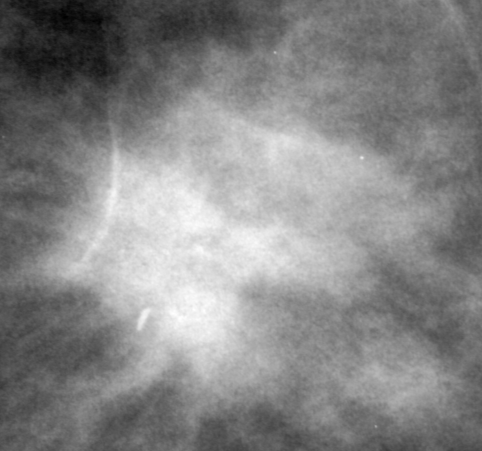
Cropped region of a digitized screen-film mammogram centred on a radiologist-marked abnormality, right breast, CC view.
Mass, shape irregular, margins obscured; BI-RADS assessment category 3; subtlety rating 3 on a 1 (subtle) to 5 (obvious) scale; pathology result (as recorded, not read from the image): malignant.